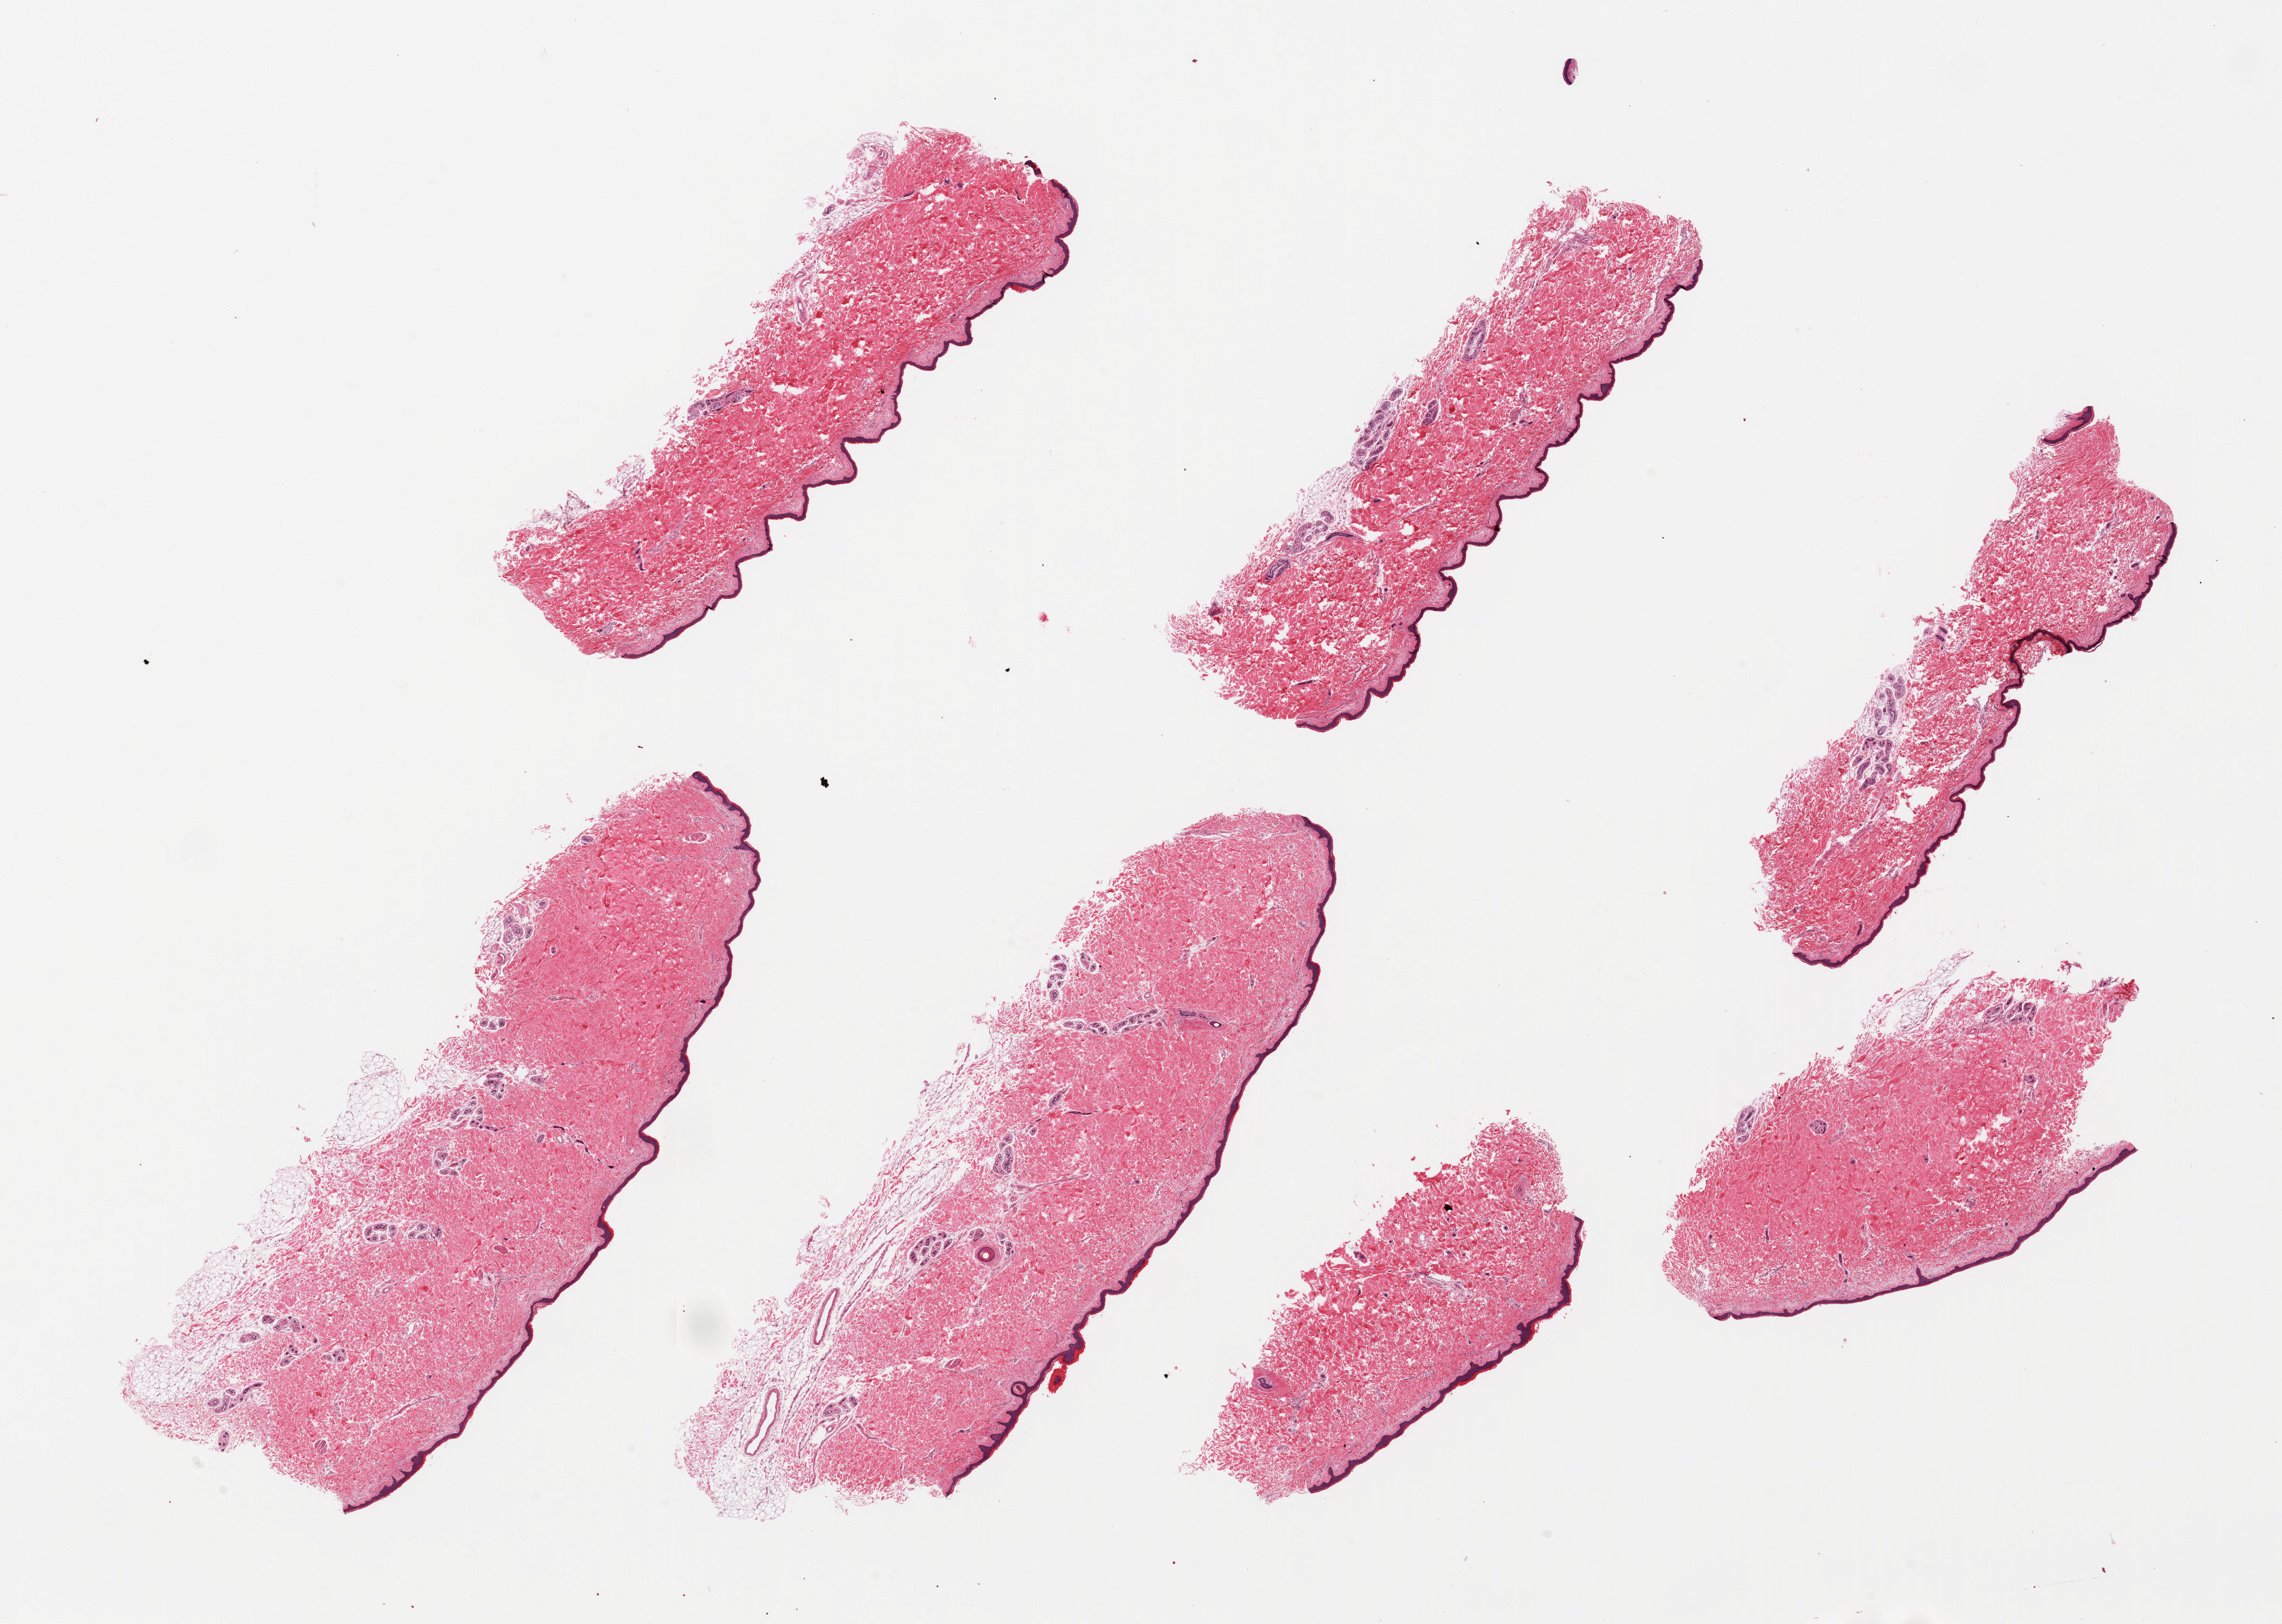
Whole-slide image, H&E stain — shown as a low-resolution overview of the whole scanned area (about 26.6 x 18.9 mm, slide scanned at 20x), PAXgene-fixed, paraffin-embedded tissue, section of skin of suprapubic region (target tissue), donor tissue sample.
Reviewer comment on this tissue sample: 7 pieces, up to 10.5x3.5mm; most subcutaneous adipose trimmed; 1 piece has <1mm adipose.